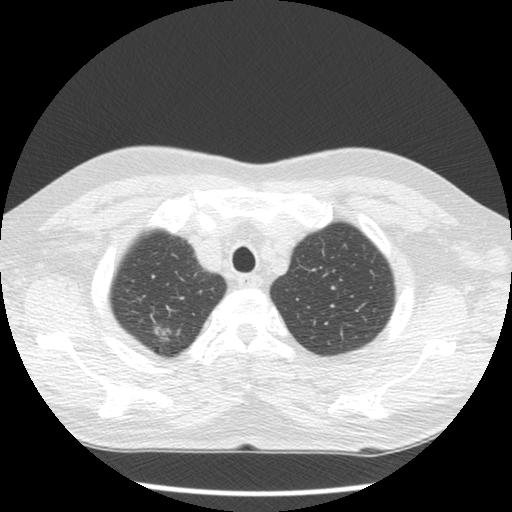
Low-dose screening chest CT, one axial slice. Position 104 of 120 along the scan axis. 120 kVp. Lung window (W 1500 / L -600 HU). 2.5 mm slice thickness. 512 × 512 image matrix, field of view 332 × 332 mm.
Annotated regions visible in this slice (expert manual segmentation):
- lesion 1 (tumor, upper lobe of right lung): bounding box <155,326,172,340> (left, top, right, bottom; pixels)